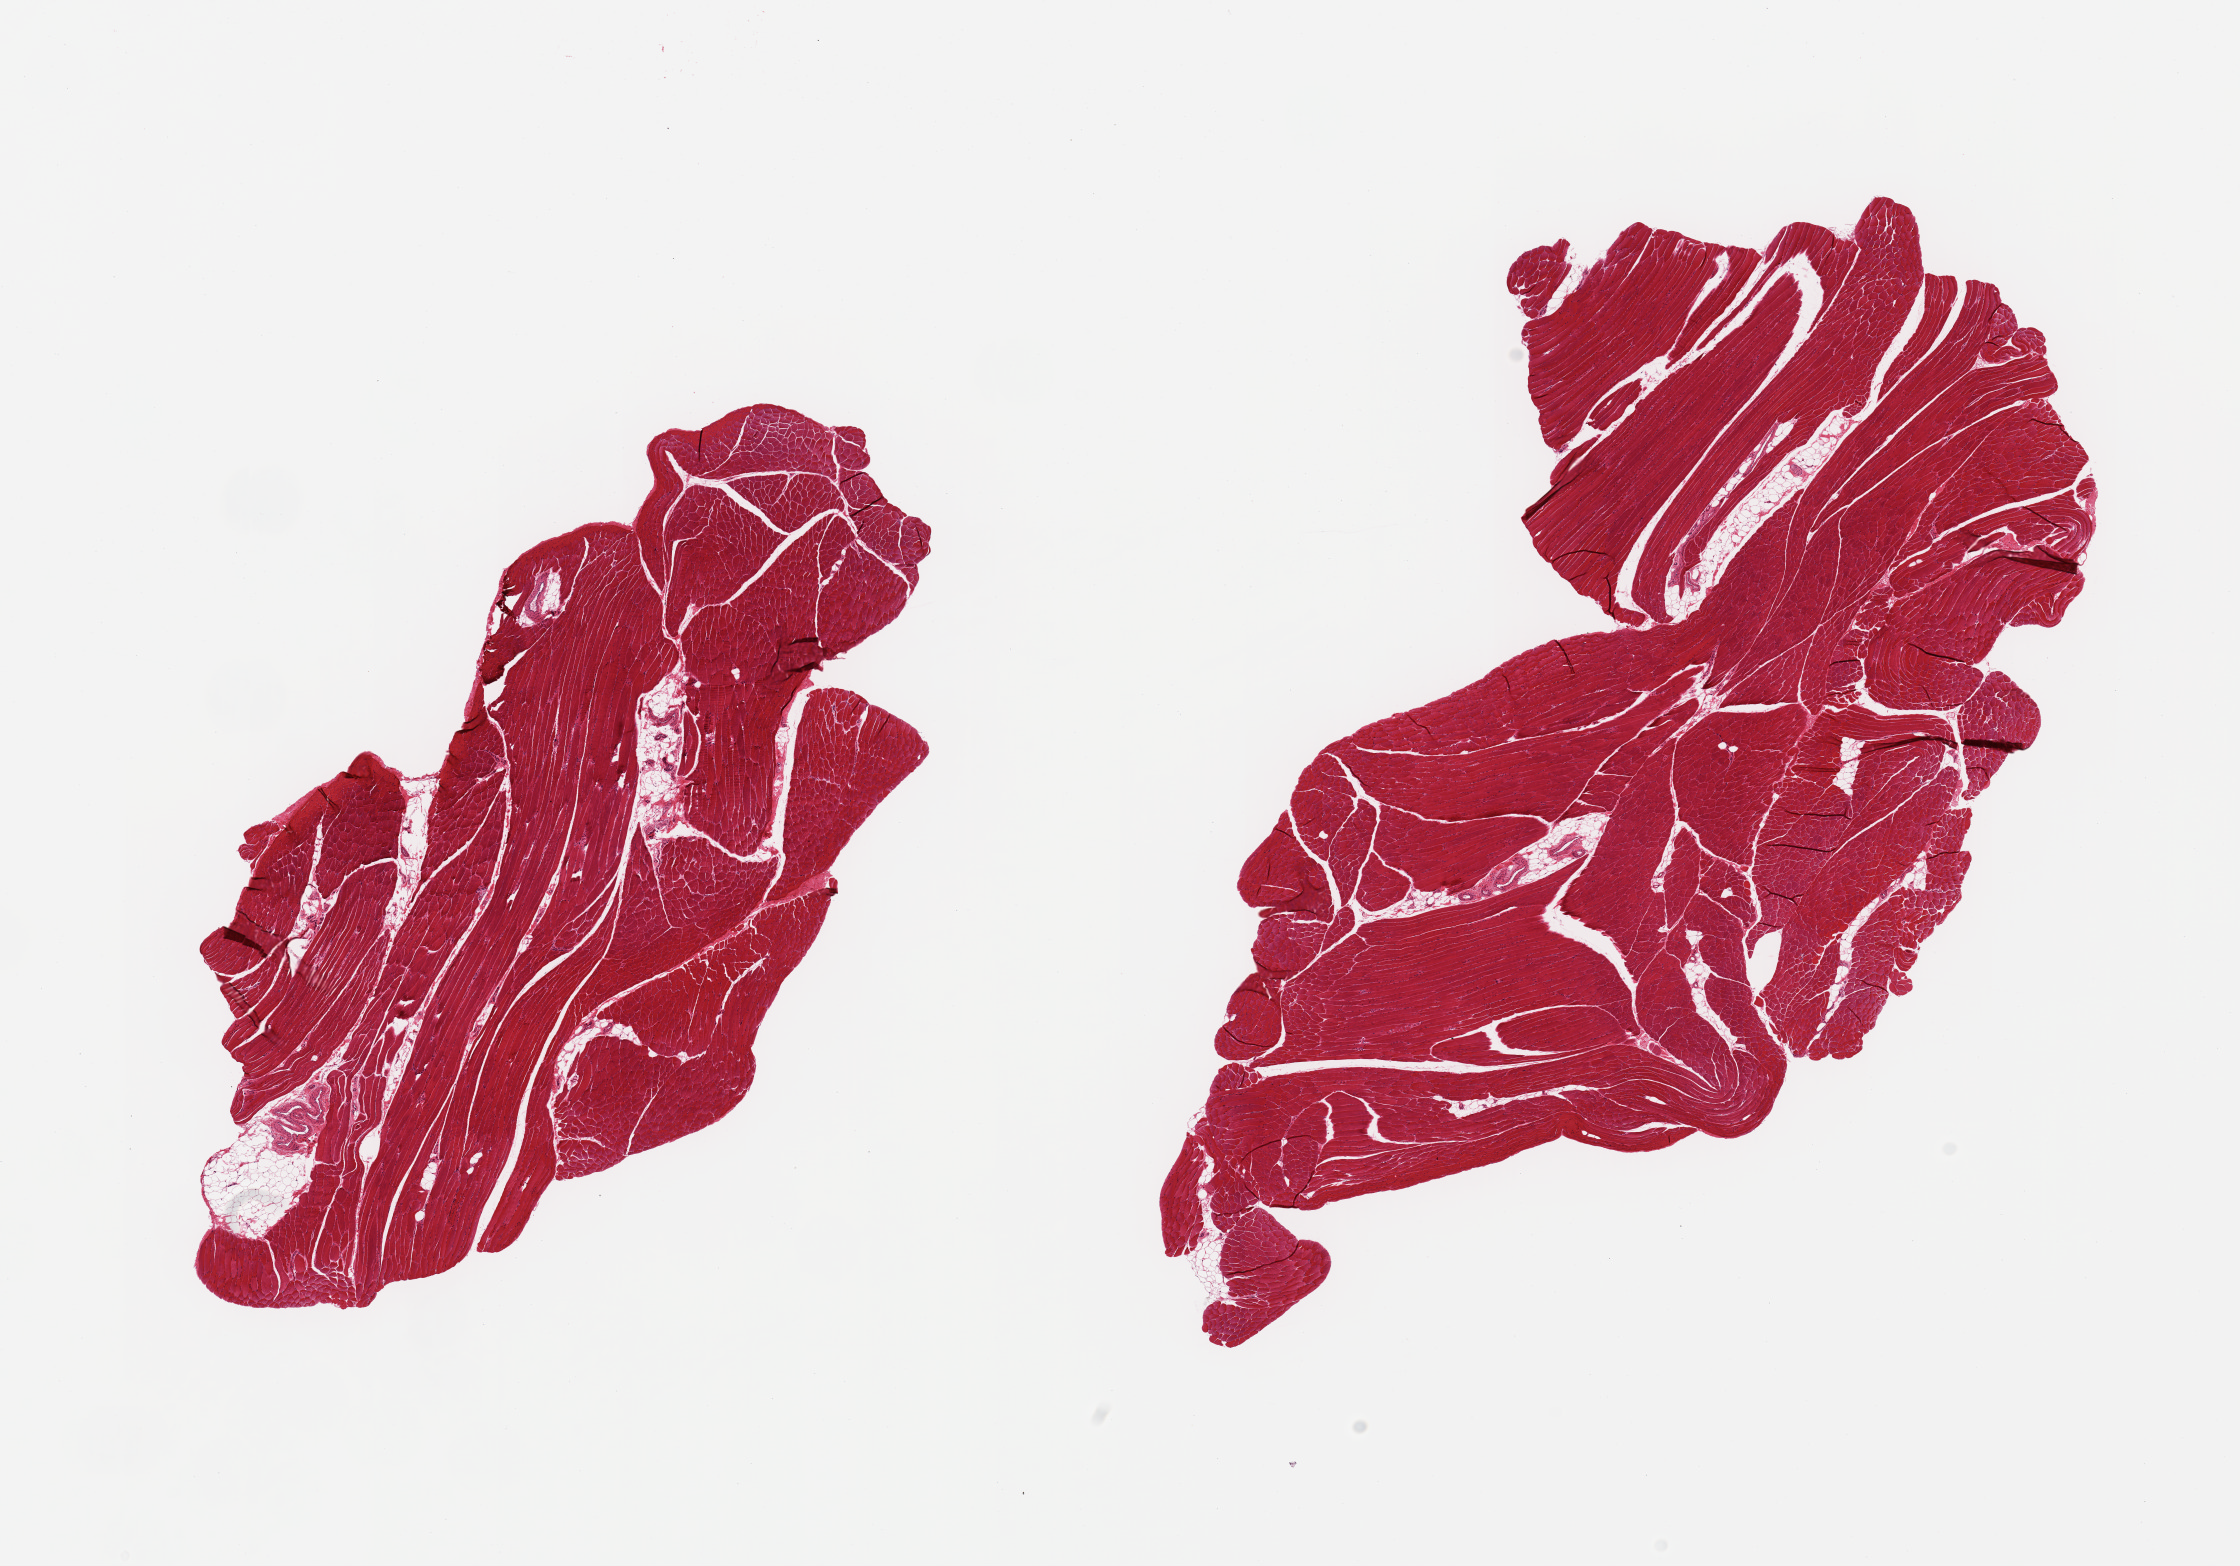
Hematoxylin and eosin (H&E) whole-slide image, brightfield, whole scanned area (about 17.7 x 12.4 mm, slide scanned at 20x) shown as a low-resolution overview, PAXgene-fixed, paraffin-embedded tissue, target tissue: skeletal muscle, tissue donor sample. Male donor.
- reviewer comment on this tissue sample: 2 pieces; ~5% of internal fat